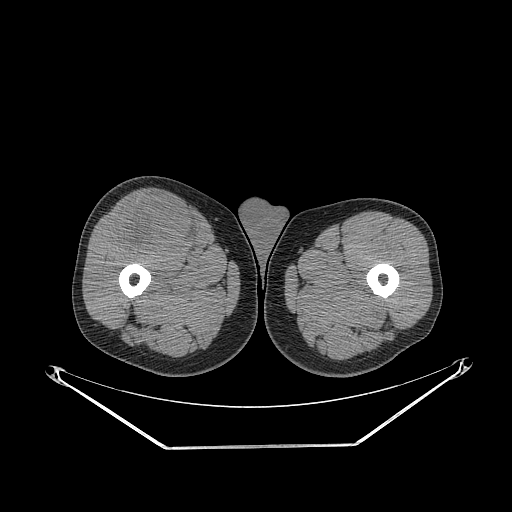
CT of an extremity soft-tissue mass (from a PET/CT study), one axial slice. Slice 276 of 311 in the series (ordered by position). Soft-tissue window (W 400 / L 40 HU). 512 × 512 image matrix, field of view 500 × 500 mm. Male patient. Case-level facts recorded for this patient, not image findings: histological type: pleiomorphic leiomyosarcoma; grade: intermediate; site of the primary tumour: right thigh.
Structures marked on this image (expert contour drawn on MRI and transferred to this co-registered scan by the dataset authors):
- gross tumour volume including surrounding oedema: box from (x=114, y=196) to (x=199, y=257) px
- gross tumour volume (mass): (x=114, y=196)–(x=199, y=257)